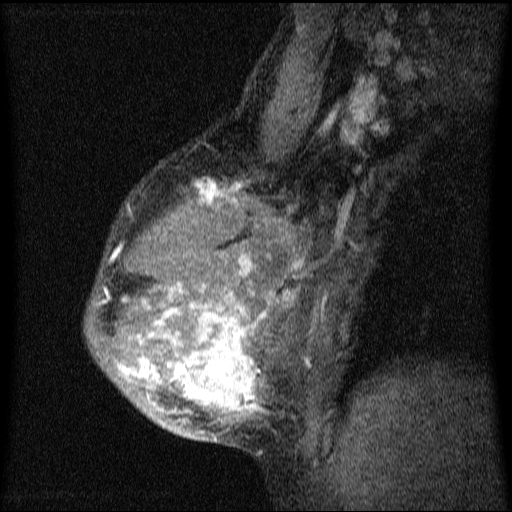
Breast MRI (dynamic contrast-enhanced), one sagittal slice. Slice 47 of 64 in the series (ordered by position). Dynamic contrast-enhanced series, image 2 of 4 at this slice position (ordered by acquisition). 1.5 T. TE 4.2 ms, TR 9.1 ms. 2 mm slice thickness. 512 × 512 image matrix. Female patient, age 33 years.
Outlined on this slice (semi-automatic segmentation, software-assisted and operator-edited):
- analysis volume of interest (the breast-tissue region the enhancement analysis was run in; not a lesion): box from (x=86, y=151) to (x=334, y=451) px
- tumour enhancement mask (voxels above the 70 % enhancement threshold inside the analysis volume of interest): (x=98, y=178)–(x=300, y=425)